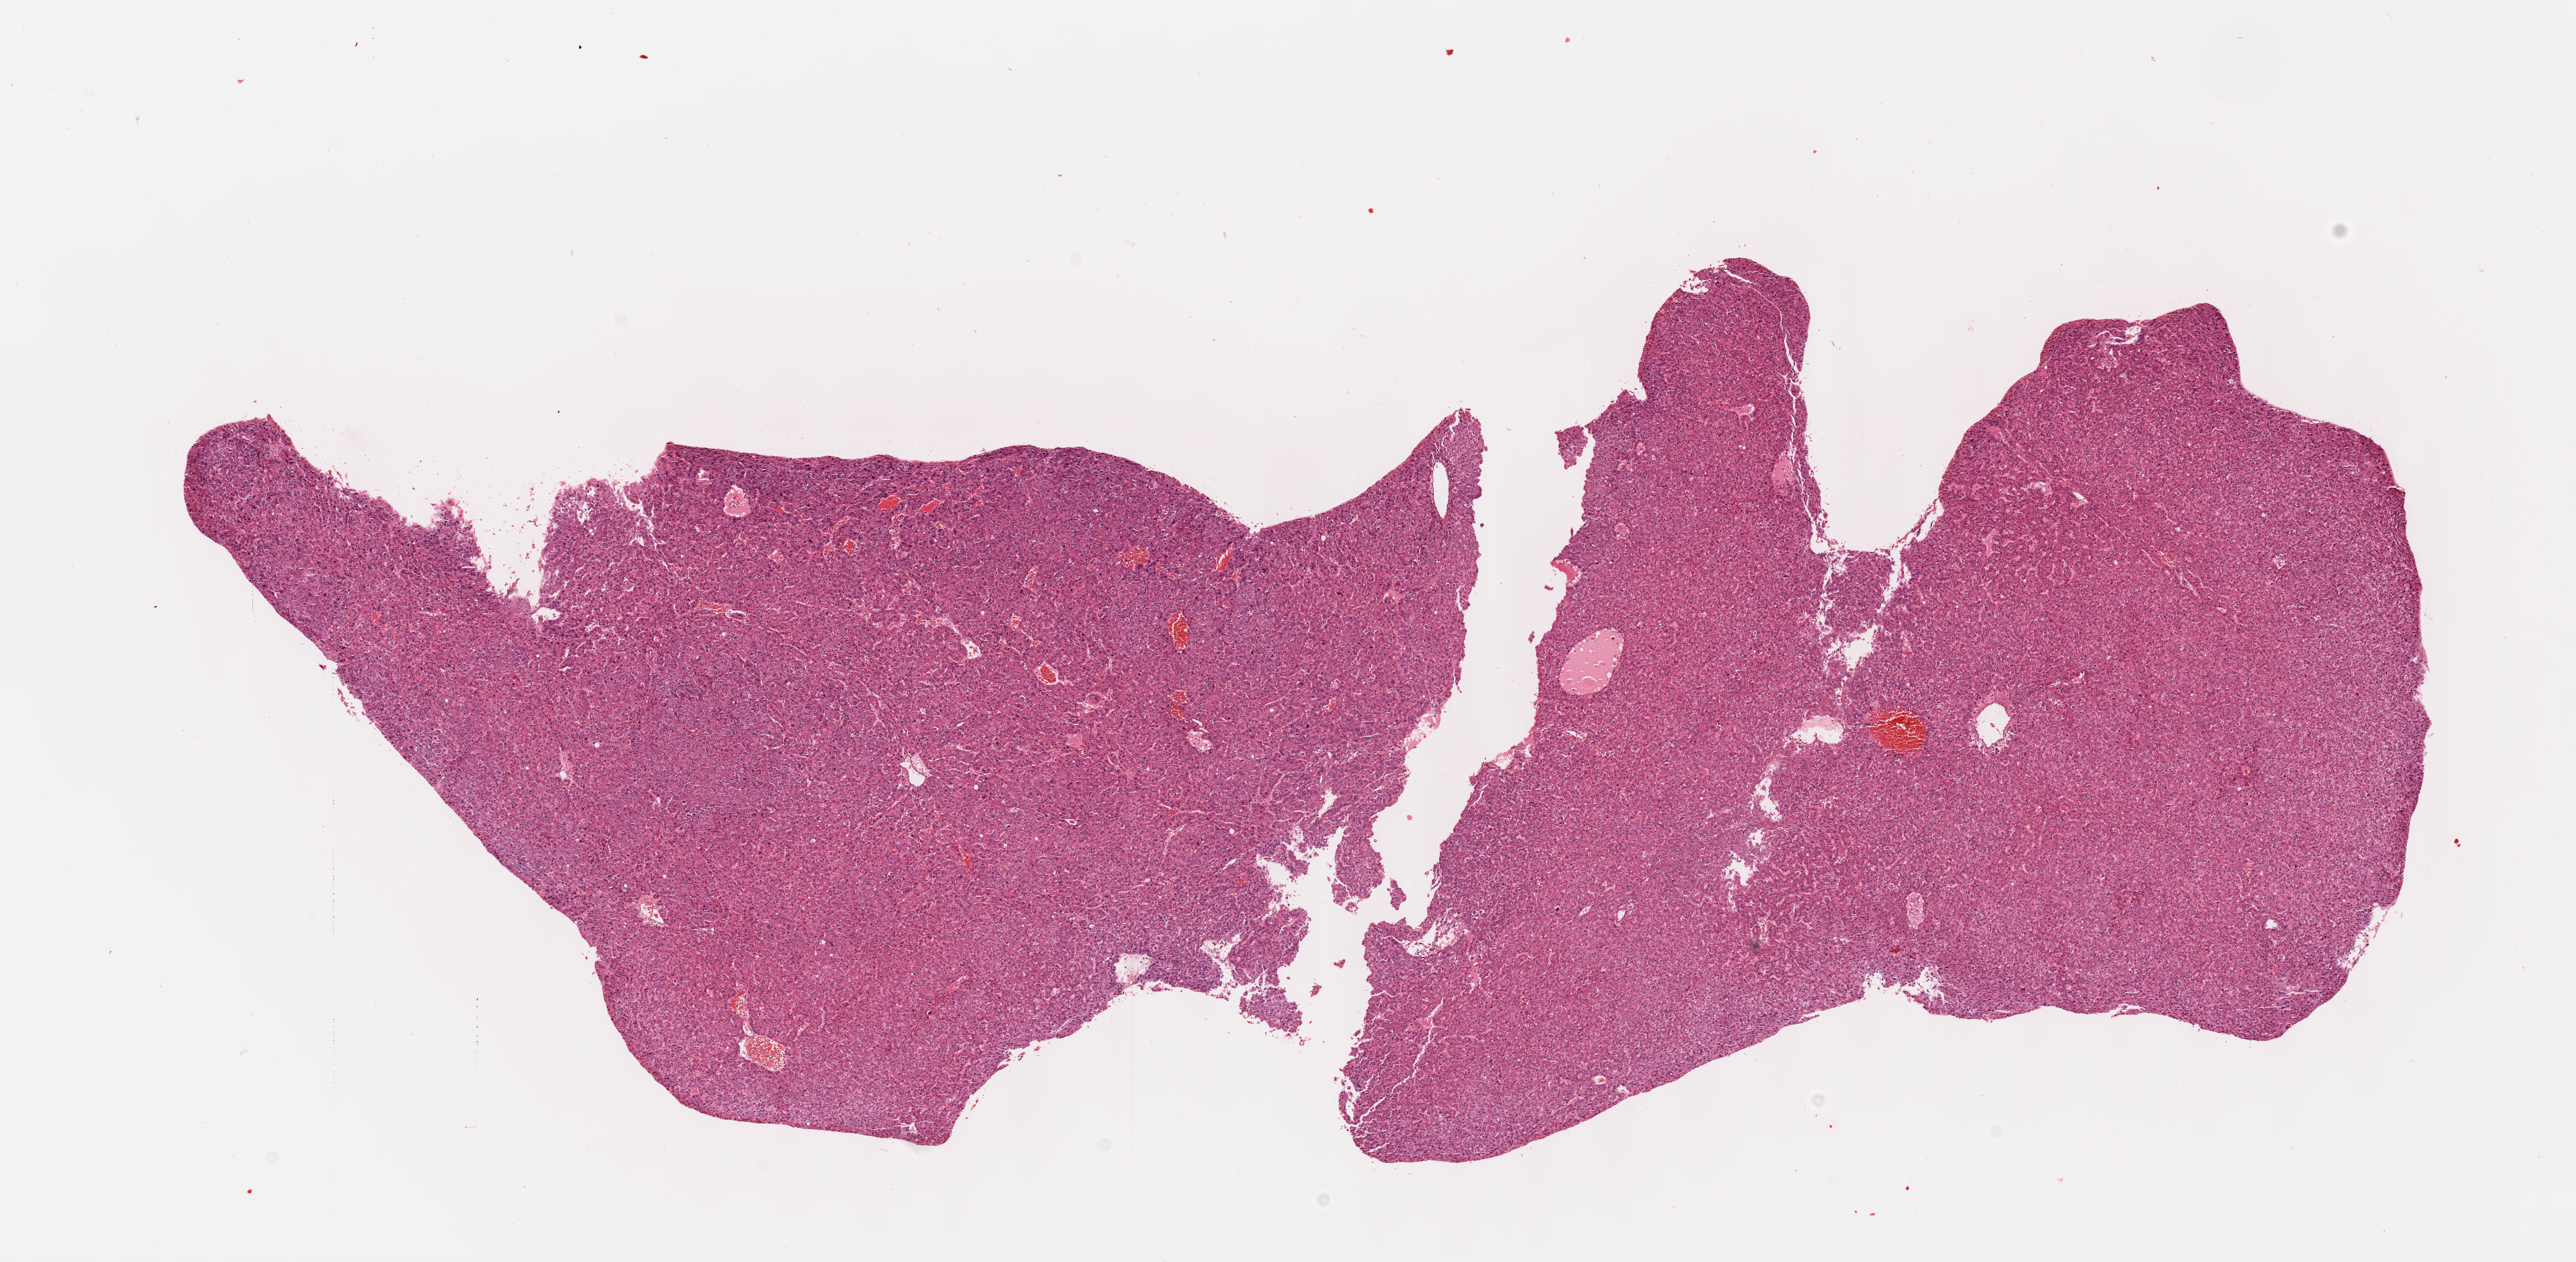
Digitized H&E tissue section (whole slide) — shown as a low-resolution overview of the whole scanned area (about 15.6 x 7.6 mm). Formalin-fixed paraffin-embedded (FFPE) diagnostic section. Sample: primary tumour, liver. Male, age 72 years at initial diagnosis.
Pathologic diagnosis: Hepatocellular carcinoma, NOS.